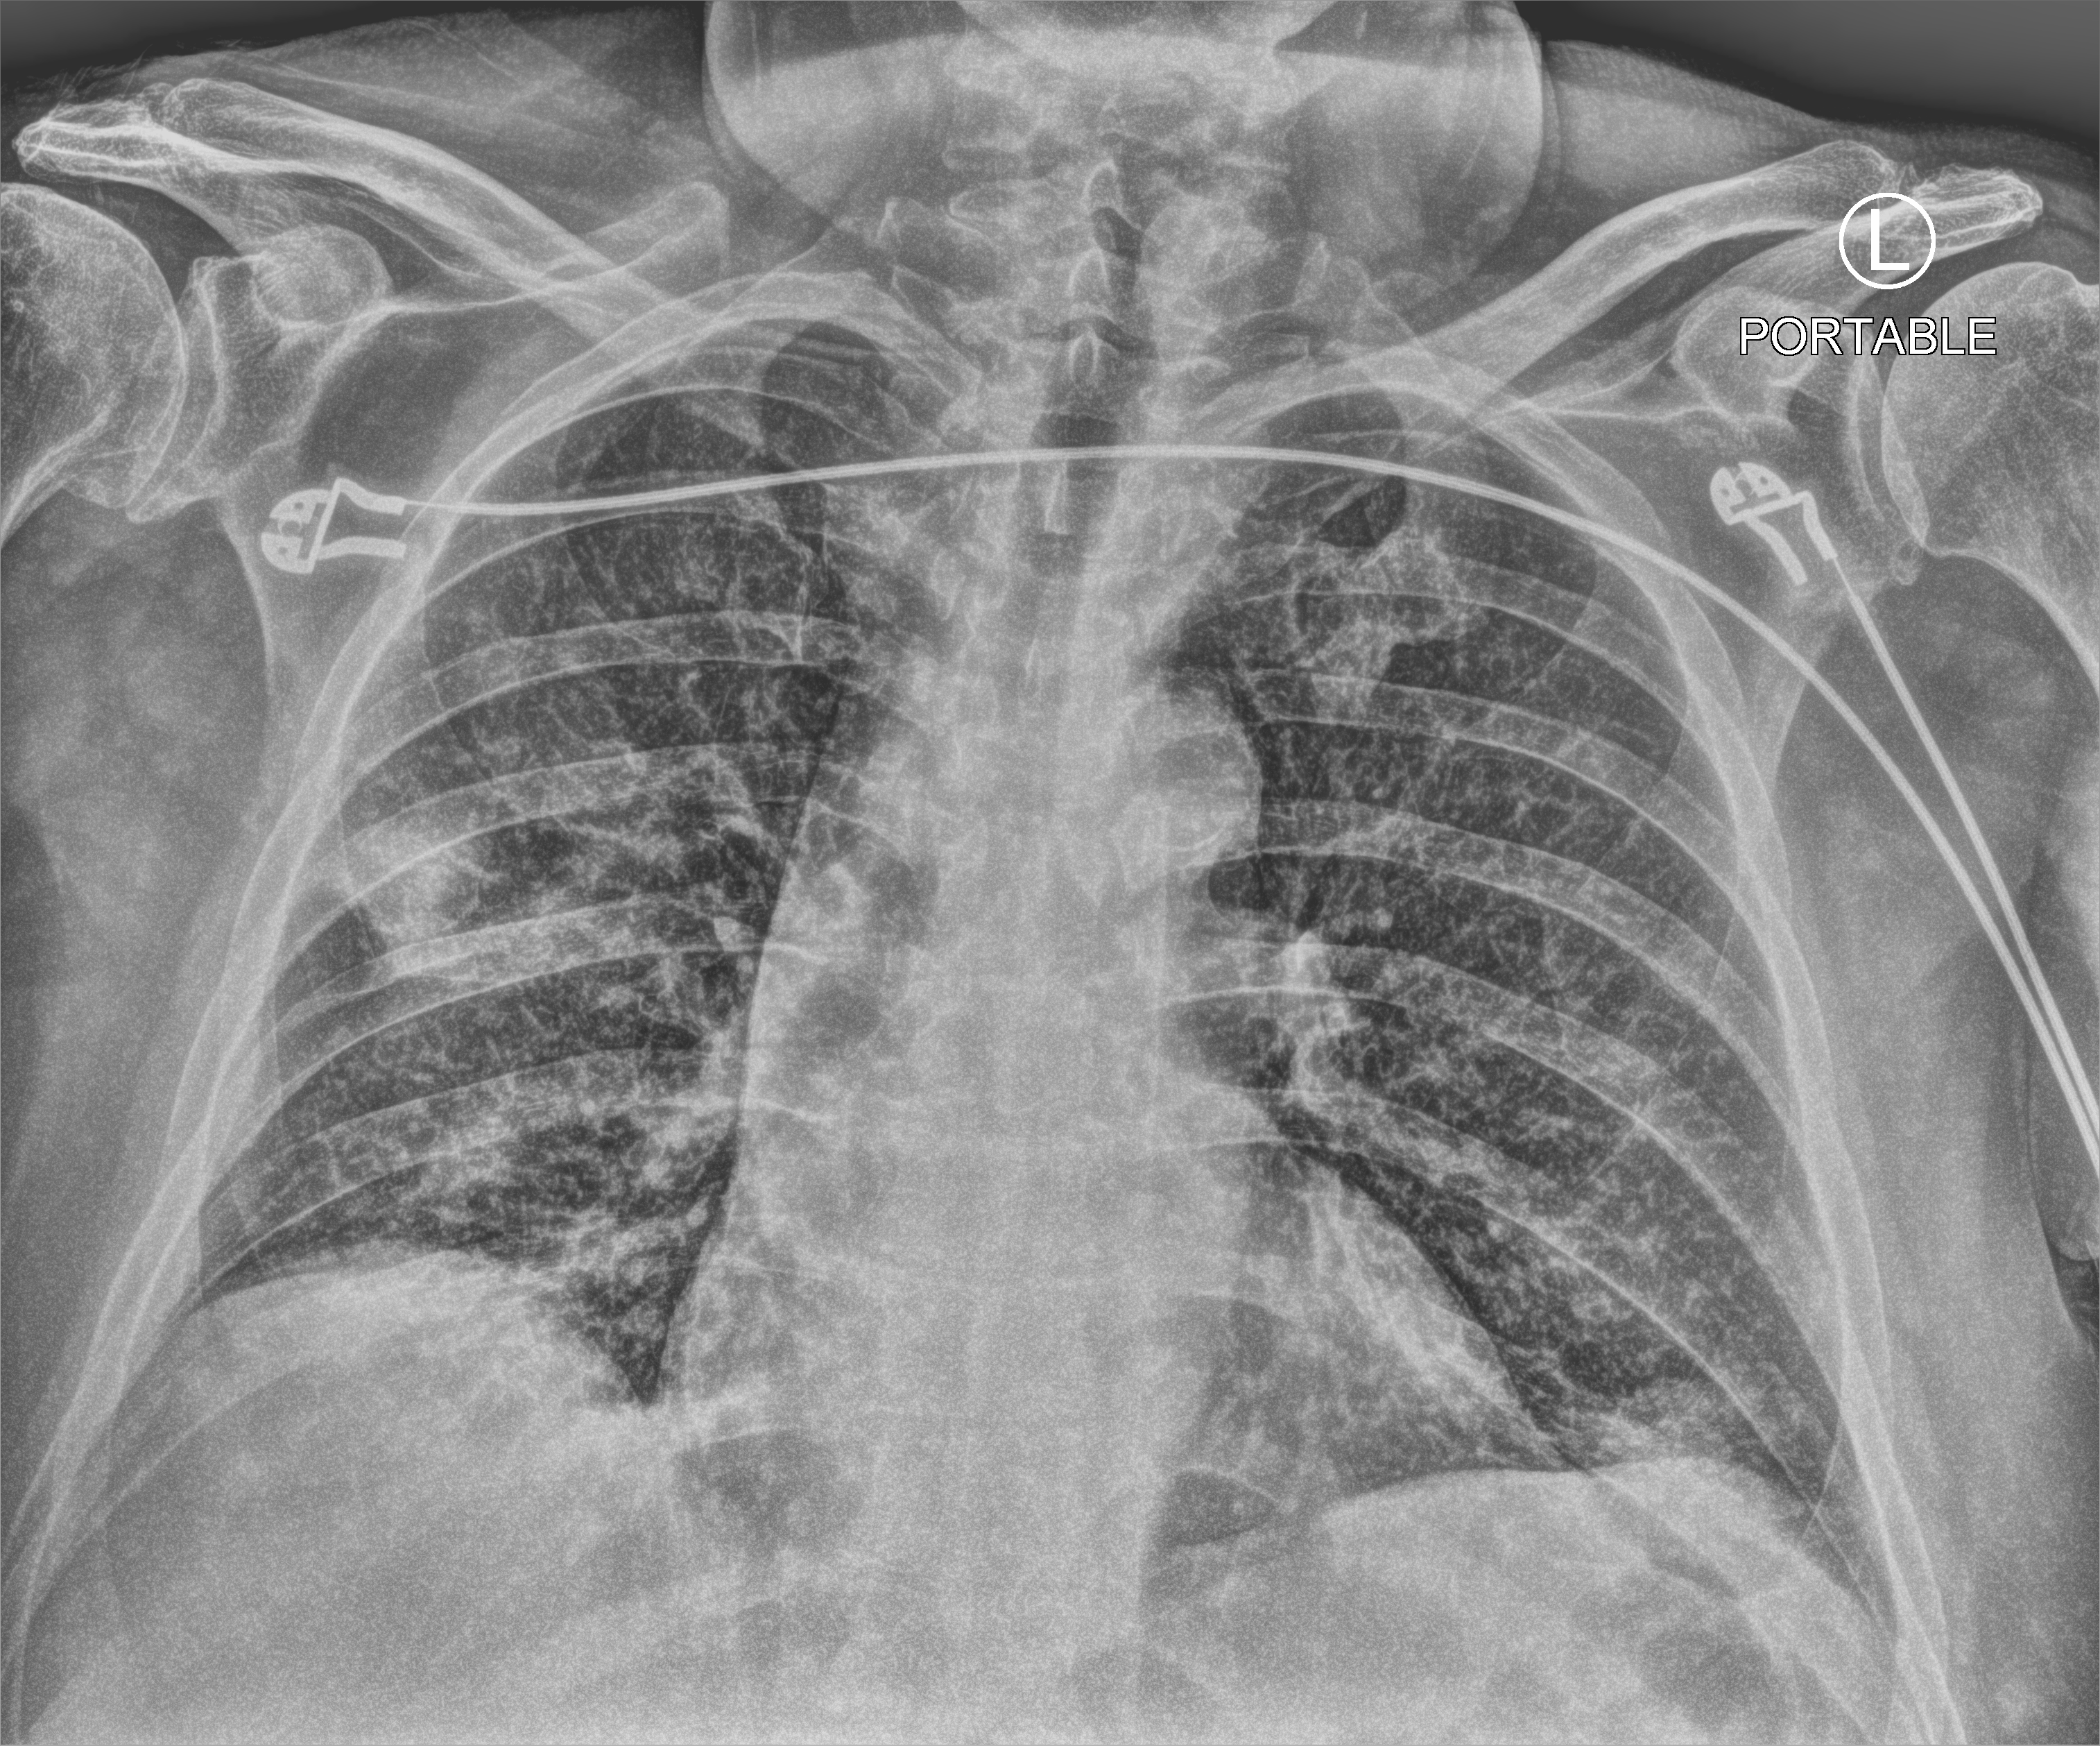
Bedside chest radiograph (computed radiography), anteroposterior (AP) projection. Patient hospitalised with COVID-19; male, aged 60–74 years.
Admission-level facts for this patient (not findings on this image; timing relative to this image not recorded): length of hospital stay: 14 days; admitted to intensive care during this hospital stay: no.